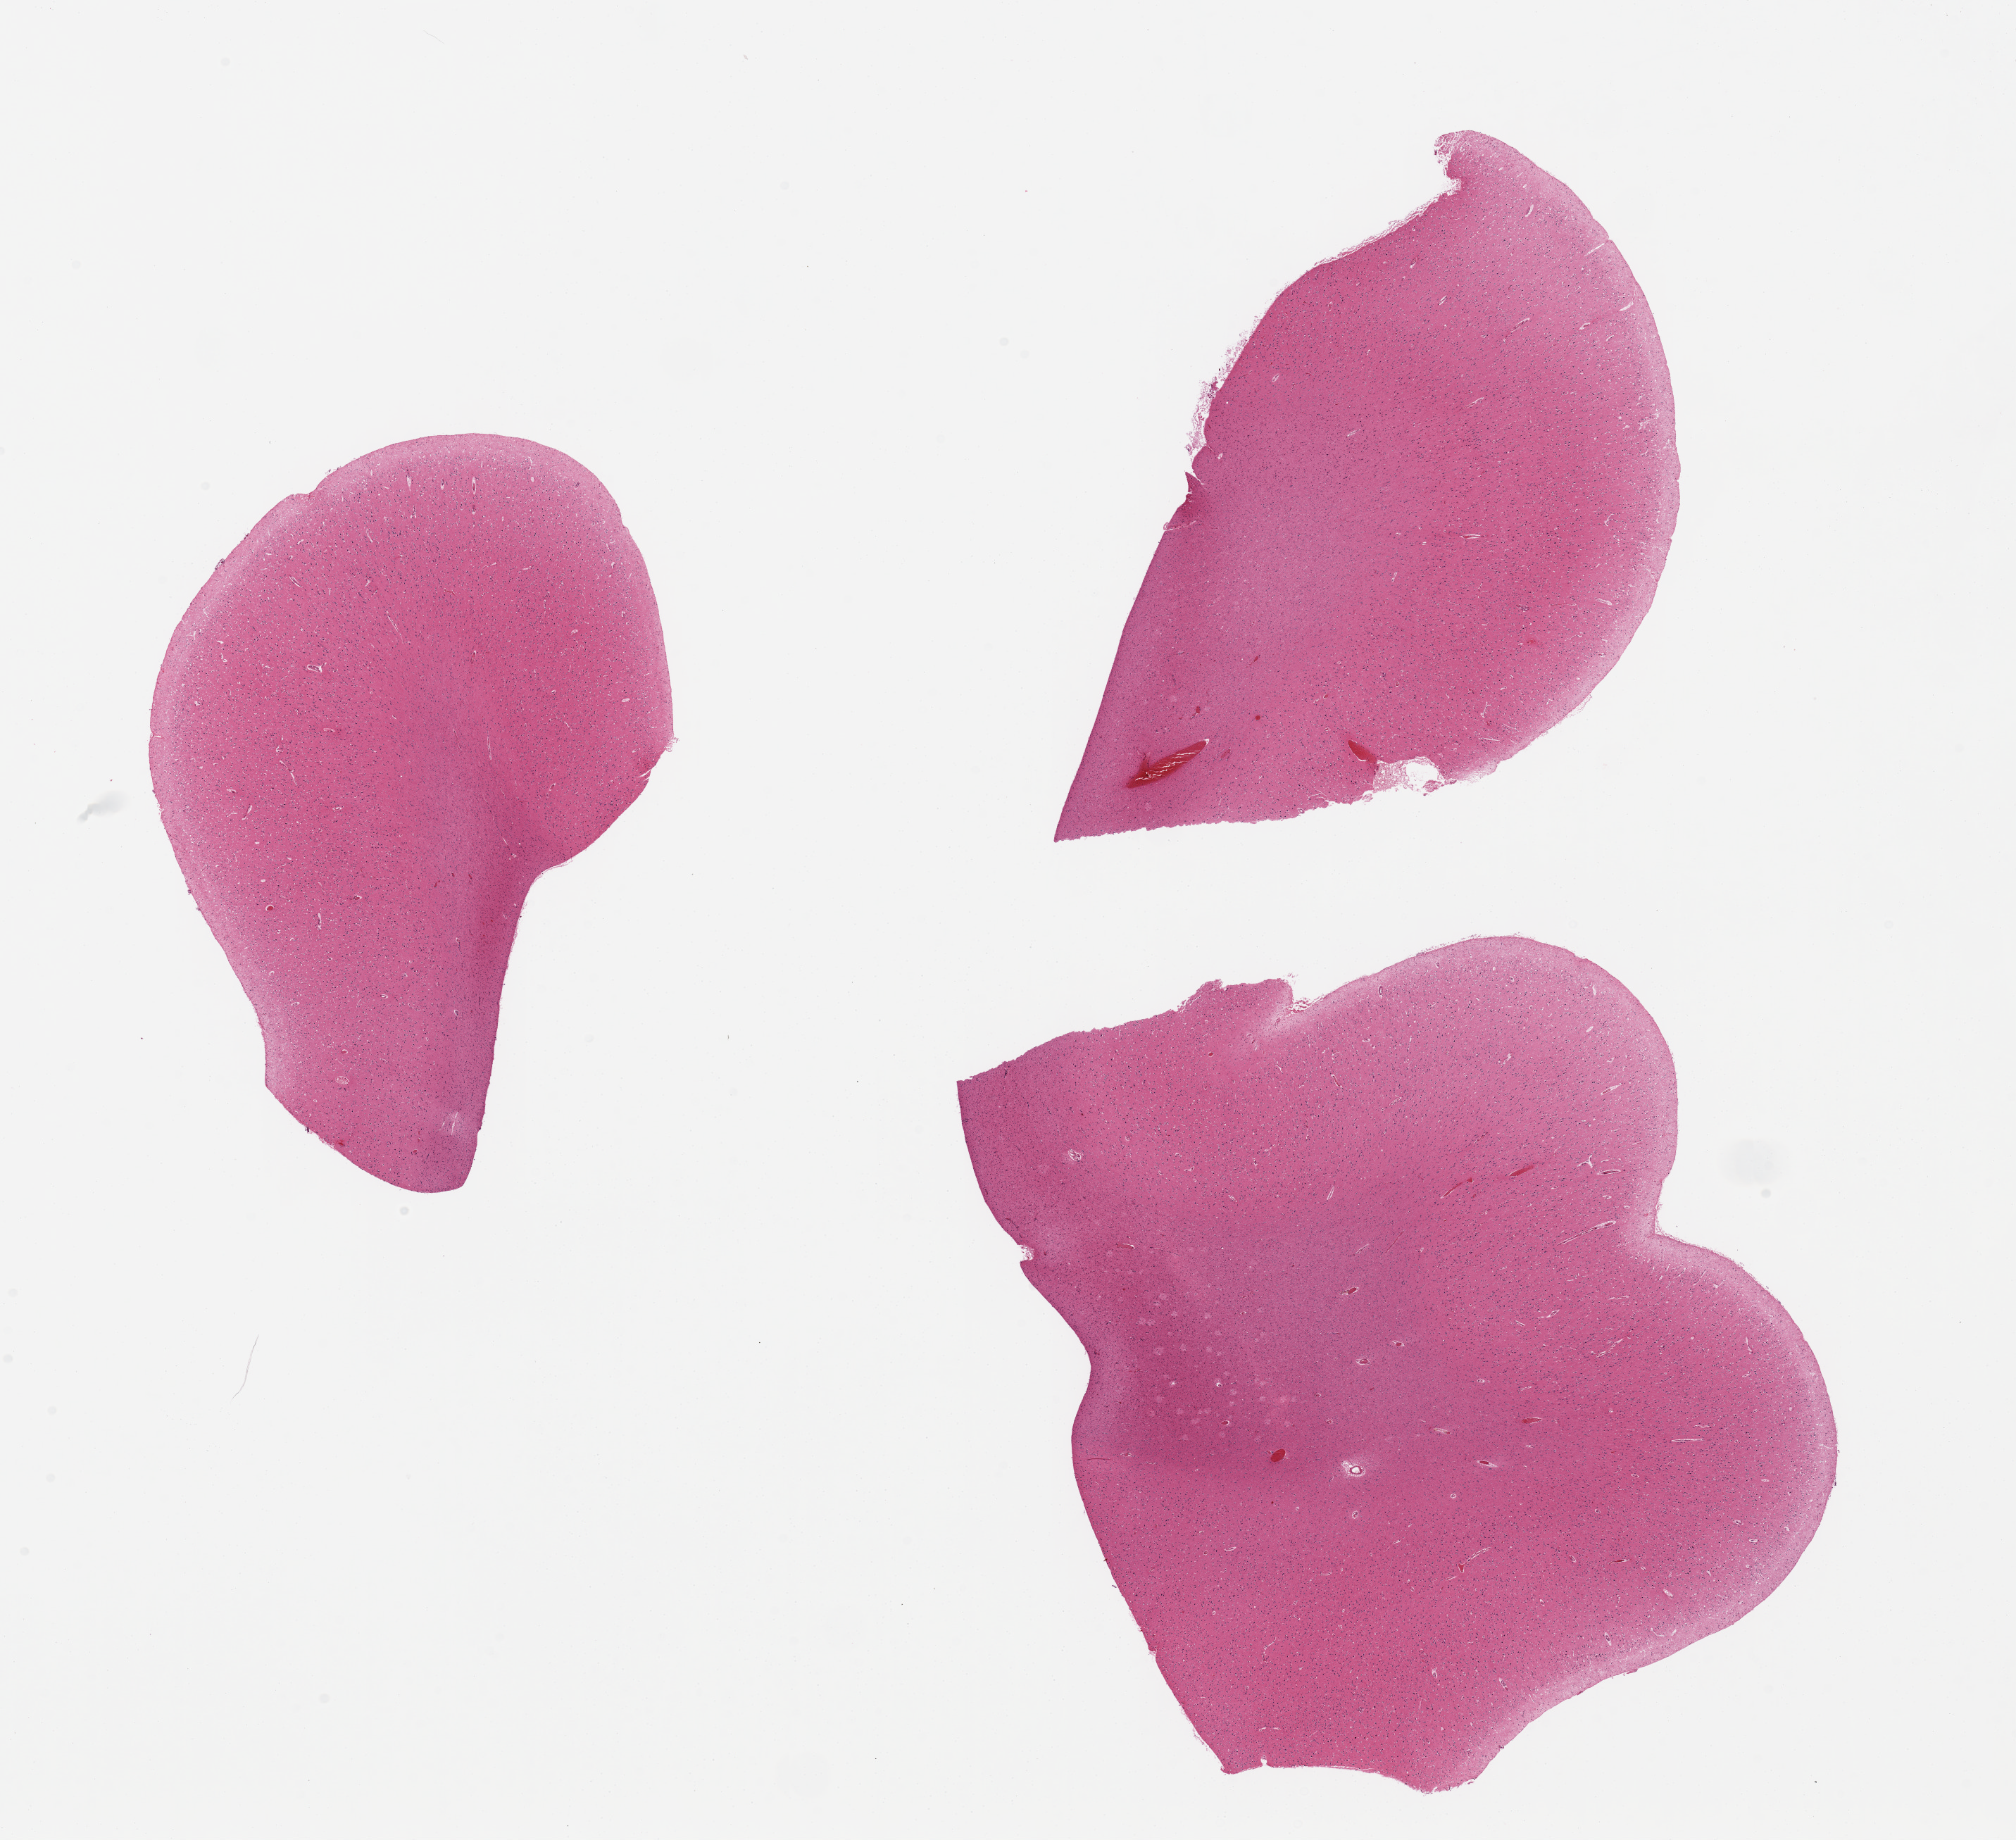
Whole-slide image, H&E stain — low-resolution overview of the scanned area, about 22.6 x 20.7 mm (acquisition: 20x scan); PAXgene-fixed paraffin-embedded (PFPE) section; section of cerebral cortex (target tissue); tissue donor sample. Donor: male.
Pathologist's review note for this sample: 3 pieces.